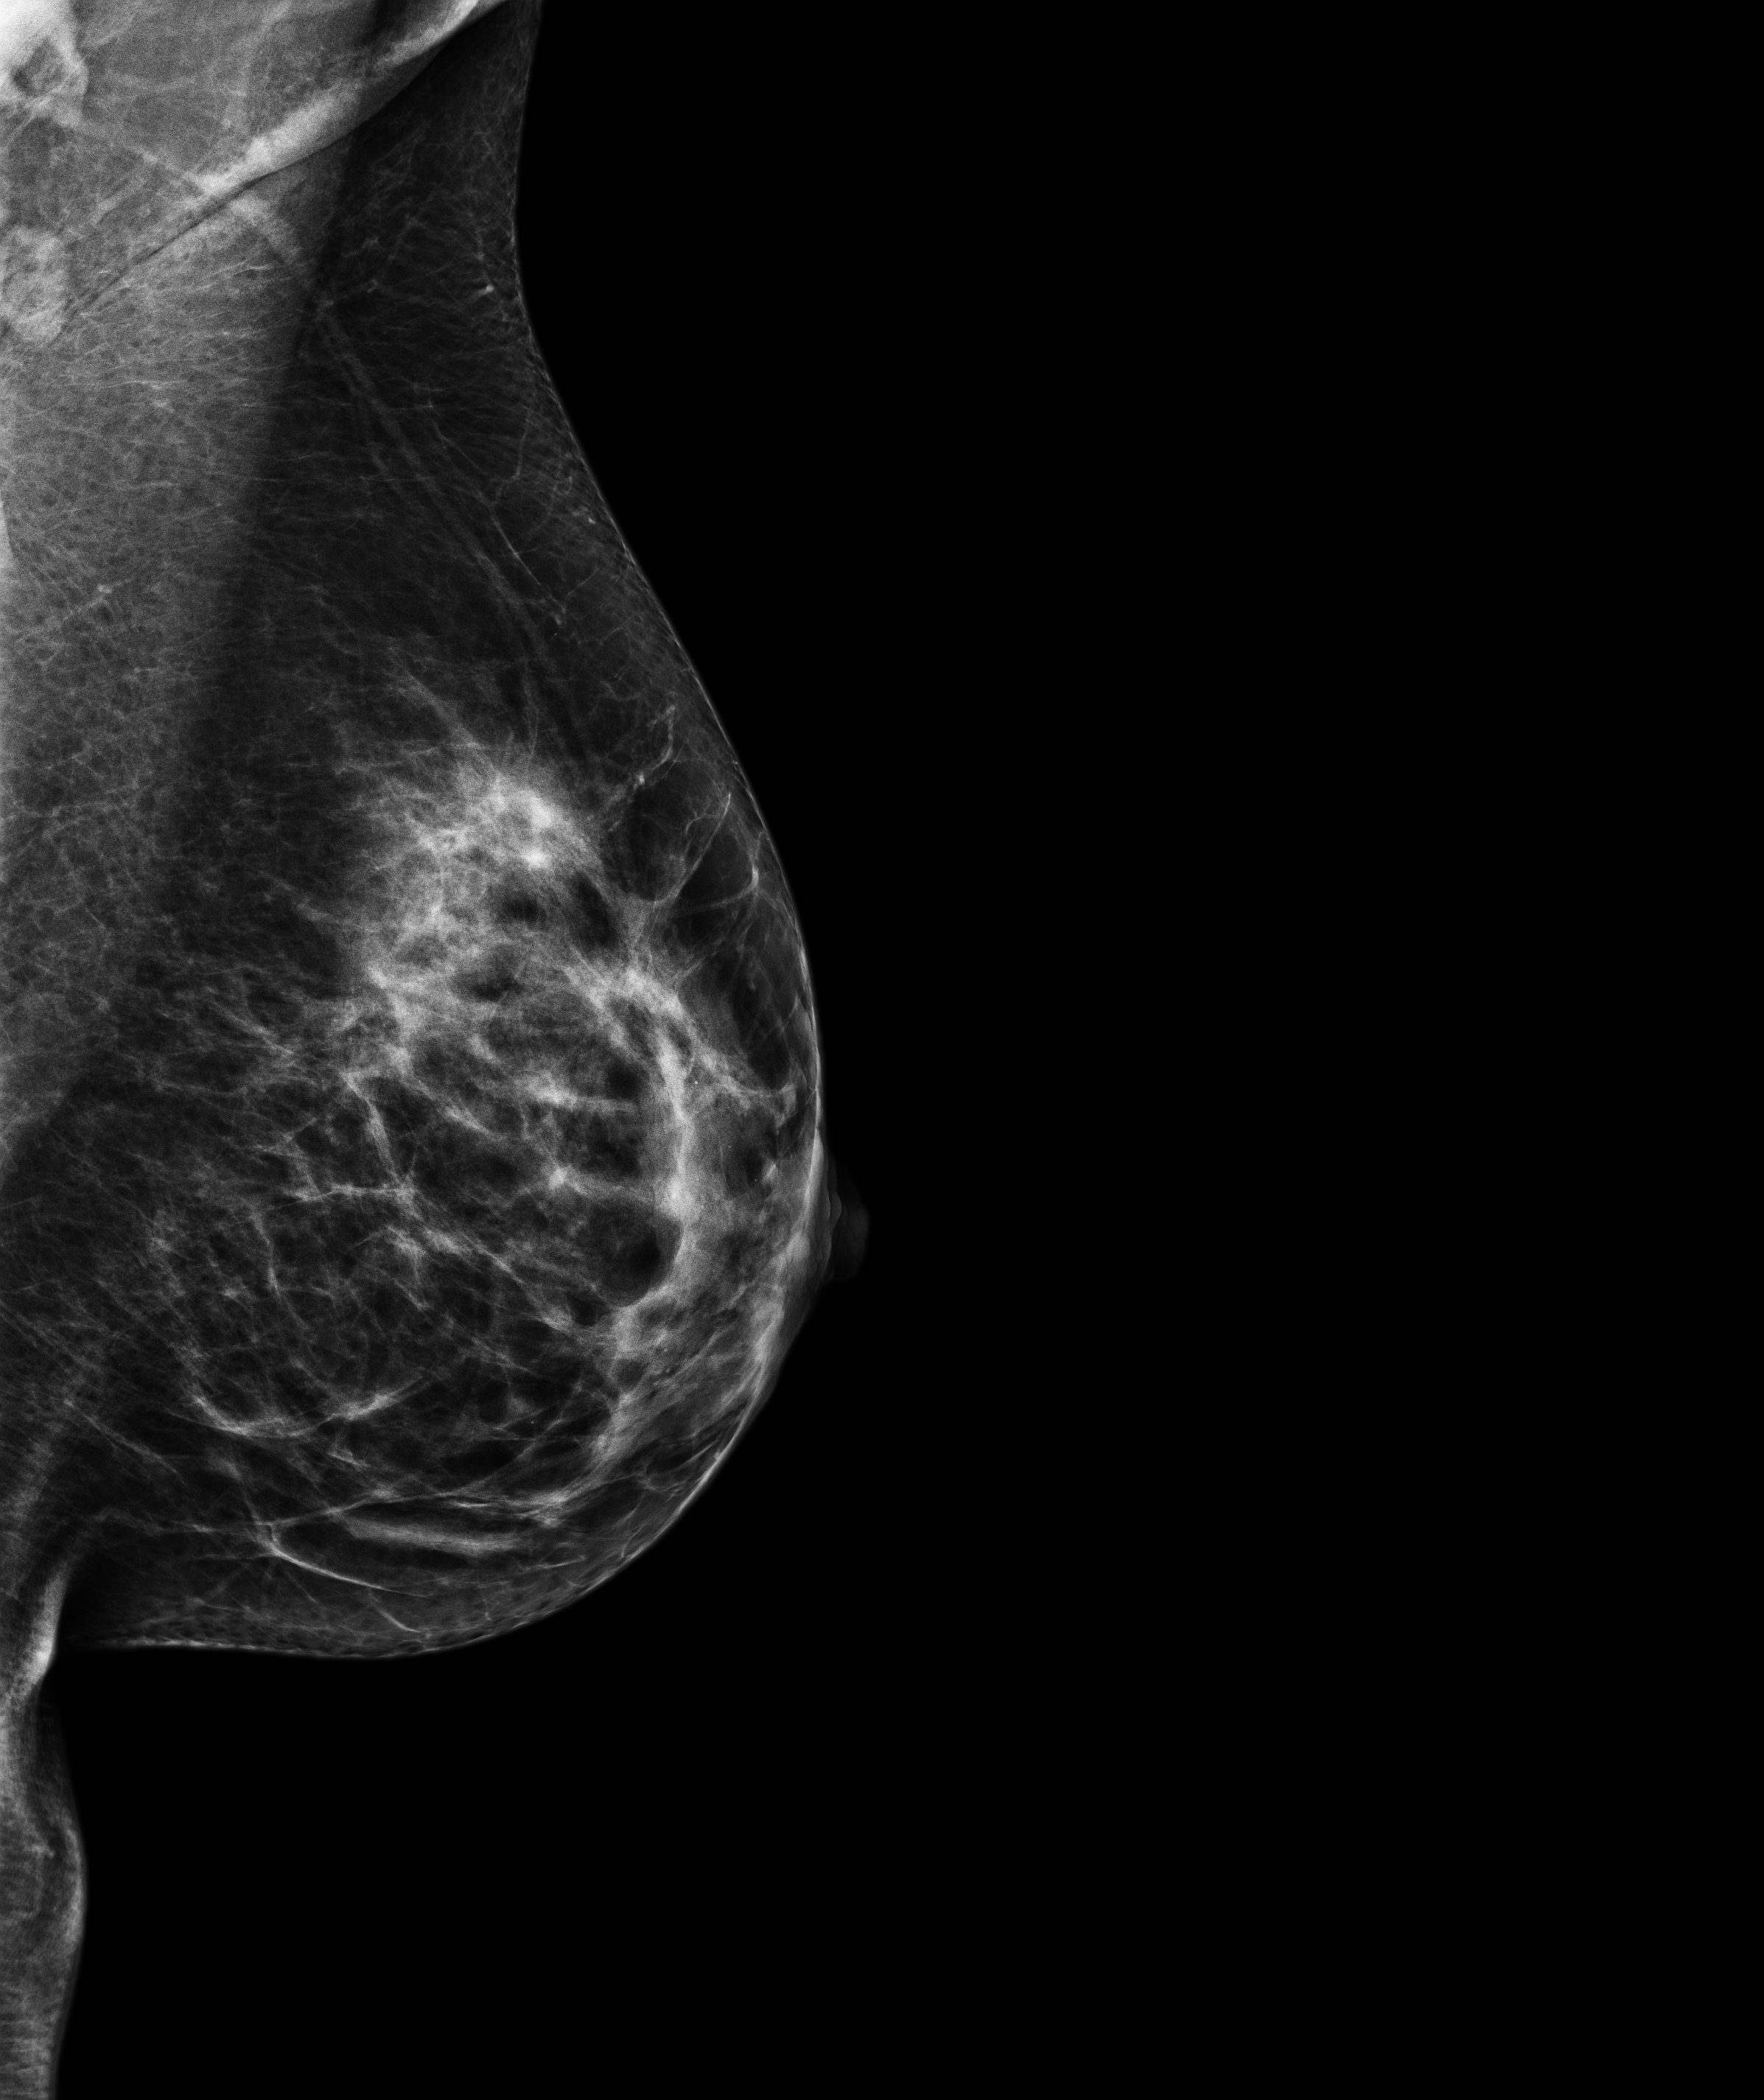
Screening examination. Patient: female, 47 years.
Image type: full-field digital mammogram. Breast: left. Projection: medio-lateral oblique projection.